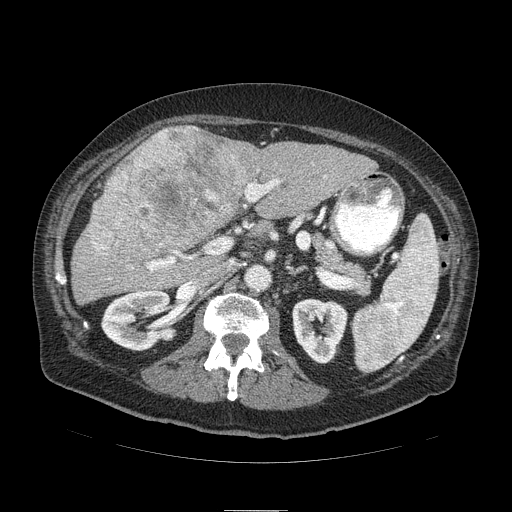
Contrast-enhanced abdominal CT (liver protocol), one axial slice. Position 45 of 103 along the scan axis. Reconstruction kernel STANDARD. 120 kVp. Soft-tissue window (W 400 / L 40 HU). 2.5 mm slice thickness. 512 × 512 image matrix, field of view 440 × 440 mm. Case-level facts recorded for this patient, not image findings: diagnosis: hepatocellular carcinoma (patient treated with transarterial chemoembolisation; whether this scan precedes or follows treatment is not stated here); TNM stage (as recorded): Stage-IIIA; Child-Pugh class: B; tumour differentiation: well differentiated.
Outlined on this slice (semi-automatically segmented with operator editing):
- liver parenchyma outside the tumour (the mass and vessels are separate outlines, so this box may not span the whole liver): bounding box (x1, y1, x2, y2) in pixels: (70, 126, 376, 304)
- mass: (87, 126, 254, 261)
- liver vessels: (147, 179, 279, 271)